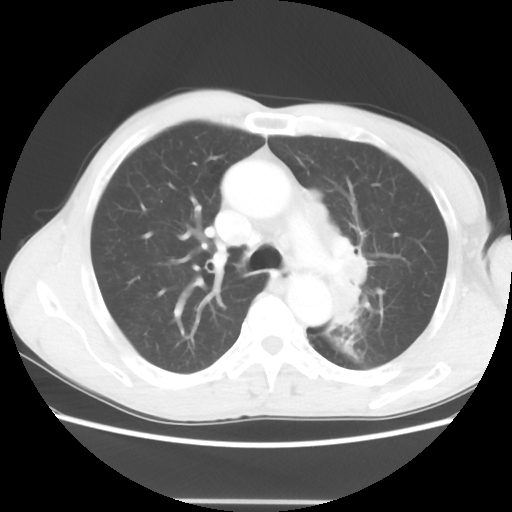
Chest CT, one axial slice. Slice 43 of 62 in the series (ordered by position). Reconstruction kernel STANDARD. 100 kVp. Lung window (W 1500 / L -600 HU). 5 mm slice thickness. 512 × 512 image matrix, field of view 360 × 360 mm. Male patient, age 61 years. Case-level facts recorded for this patient, not image findings: clinical TNM (as recorded): T3 N1 M1.
Outlined on this slice (rectangle marked by the reading radiologist):
- lung tumour (recorded histology: adenocarcinoma): bounding box (x1, y1, x2, y2) in pixels: (299, 183, 370, 333)